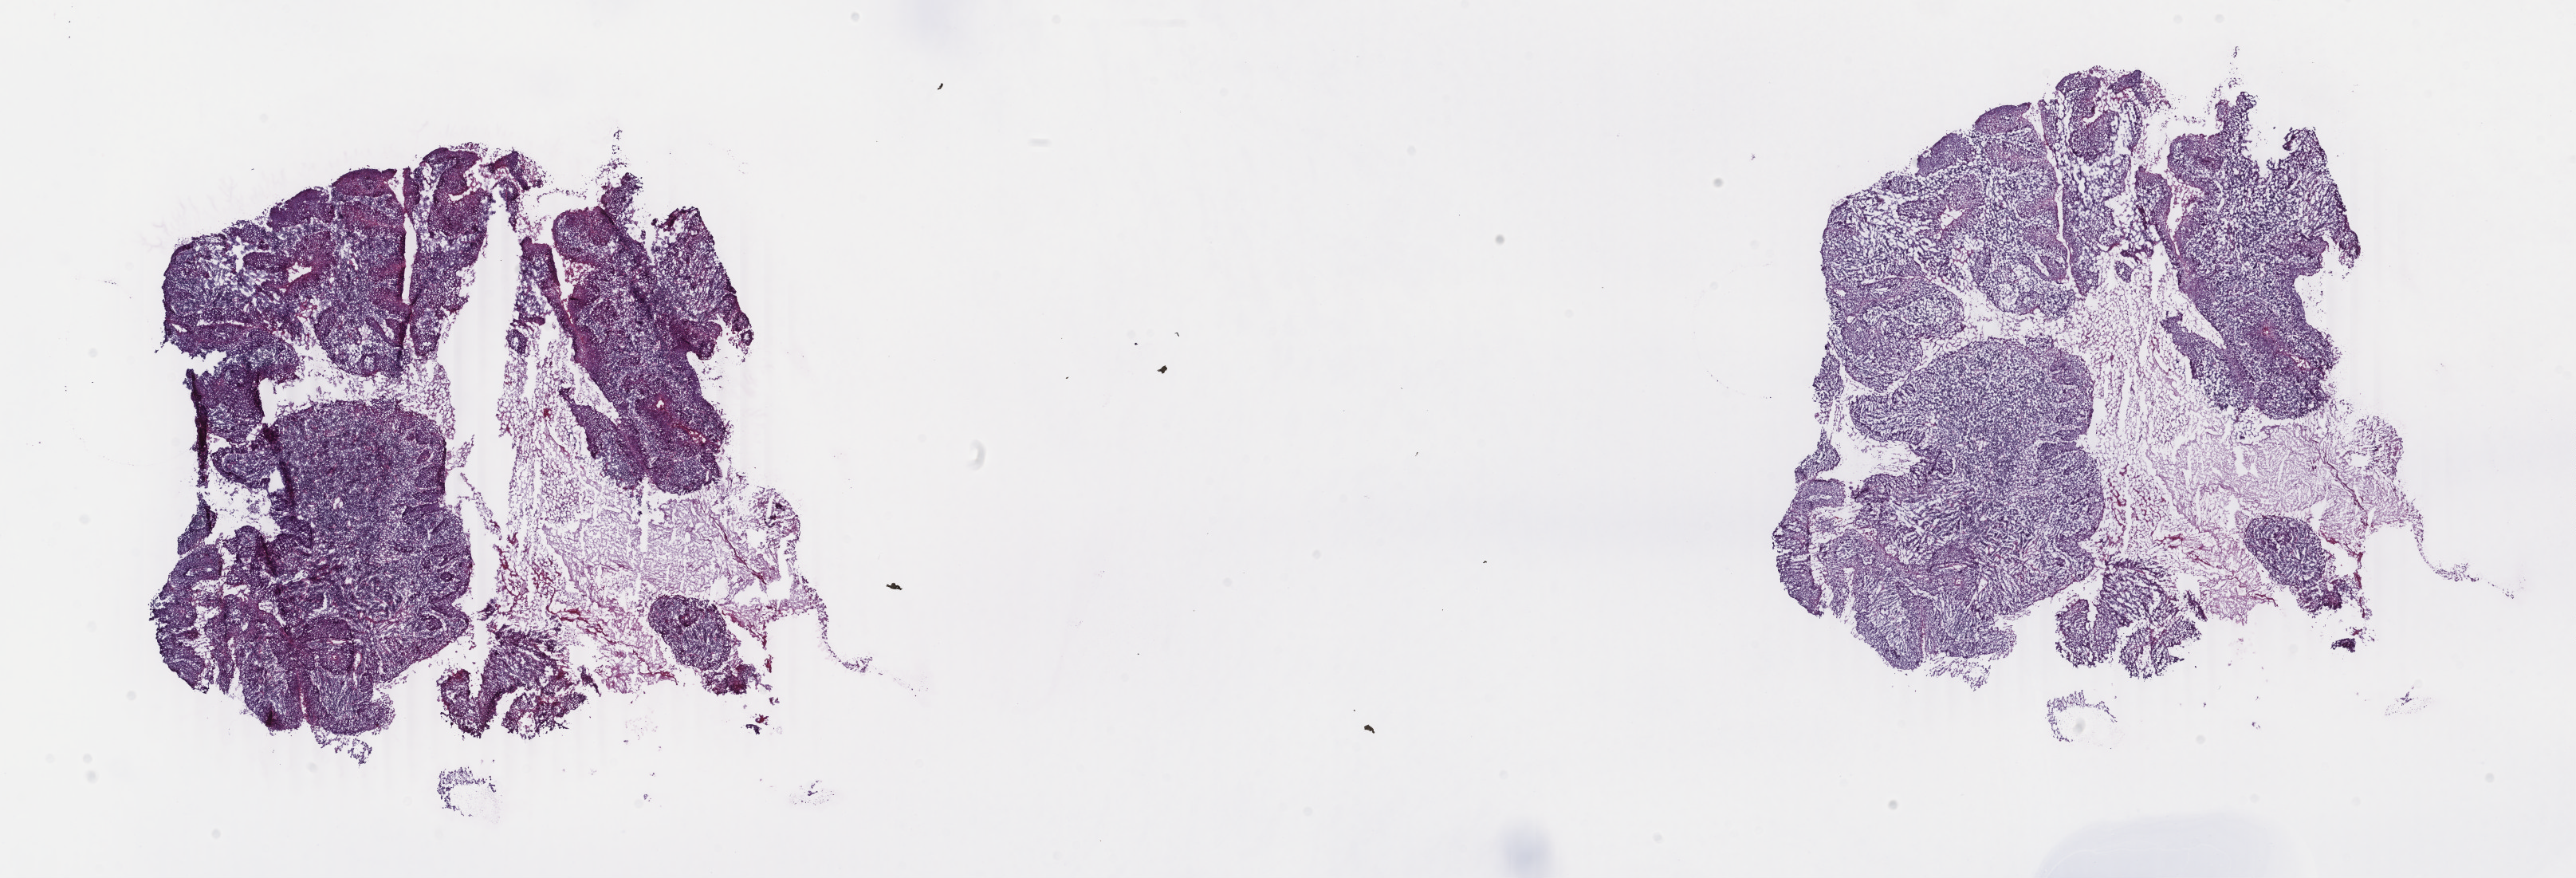
Digitized H&E-stained tissue section (whole slide) — low-resolution overview of the scanned area, about 25.7 x 8.8 mm; frozen section from the top of the tissue portion; cervix, primary tumour sample. Female, age 51 years at initial diagnosis. Histologic grade: G2 (moderately differentiated). Slide review estimates, as recorded: tumour cells 85%, tumour nuclei 95%, normal cells 0%, stromal cells 15%, necrosis 0%. Inflammatory infiltration, as recorded: lymphocyte infiltration 0%, monocyte infiltration 0%, neutrophil infiltration 0%.
Diagnosis: Squamous cell carcinoma, large cell, nonkeratinizing, NOS (cervix uteri). FIGO stage: IIB.